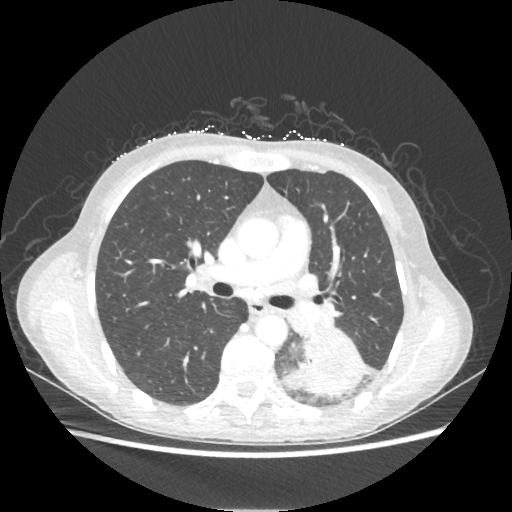
Chest CT, one axial slice; position 127 of 221 along the scan axis; reconstruction kernel STANDARD; 80 kVp; lung window (W 1500 / L -600 HU); 1.25 mm slice thickness; 512 × 512 image matrix, field of view 360 × 360 mm. Female patient, age 53 years. From the clinical record (not read from this slice): clinical TNM (as recorded): T3 N0 M0.
Outlined on this slice (rectangle marked by the reading radiologist):
- lung tumour (recorded histology: adenocarcinoma): box from (x=298, y=333) to (x=365, y=397) px